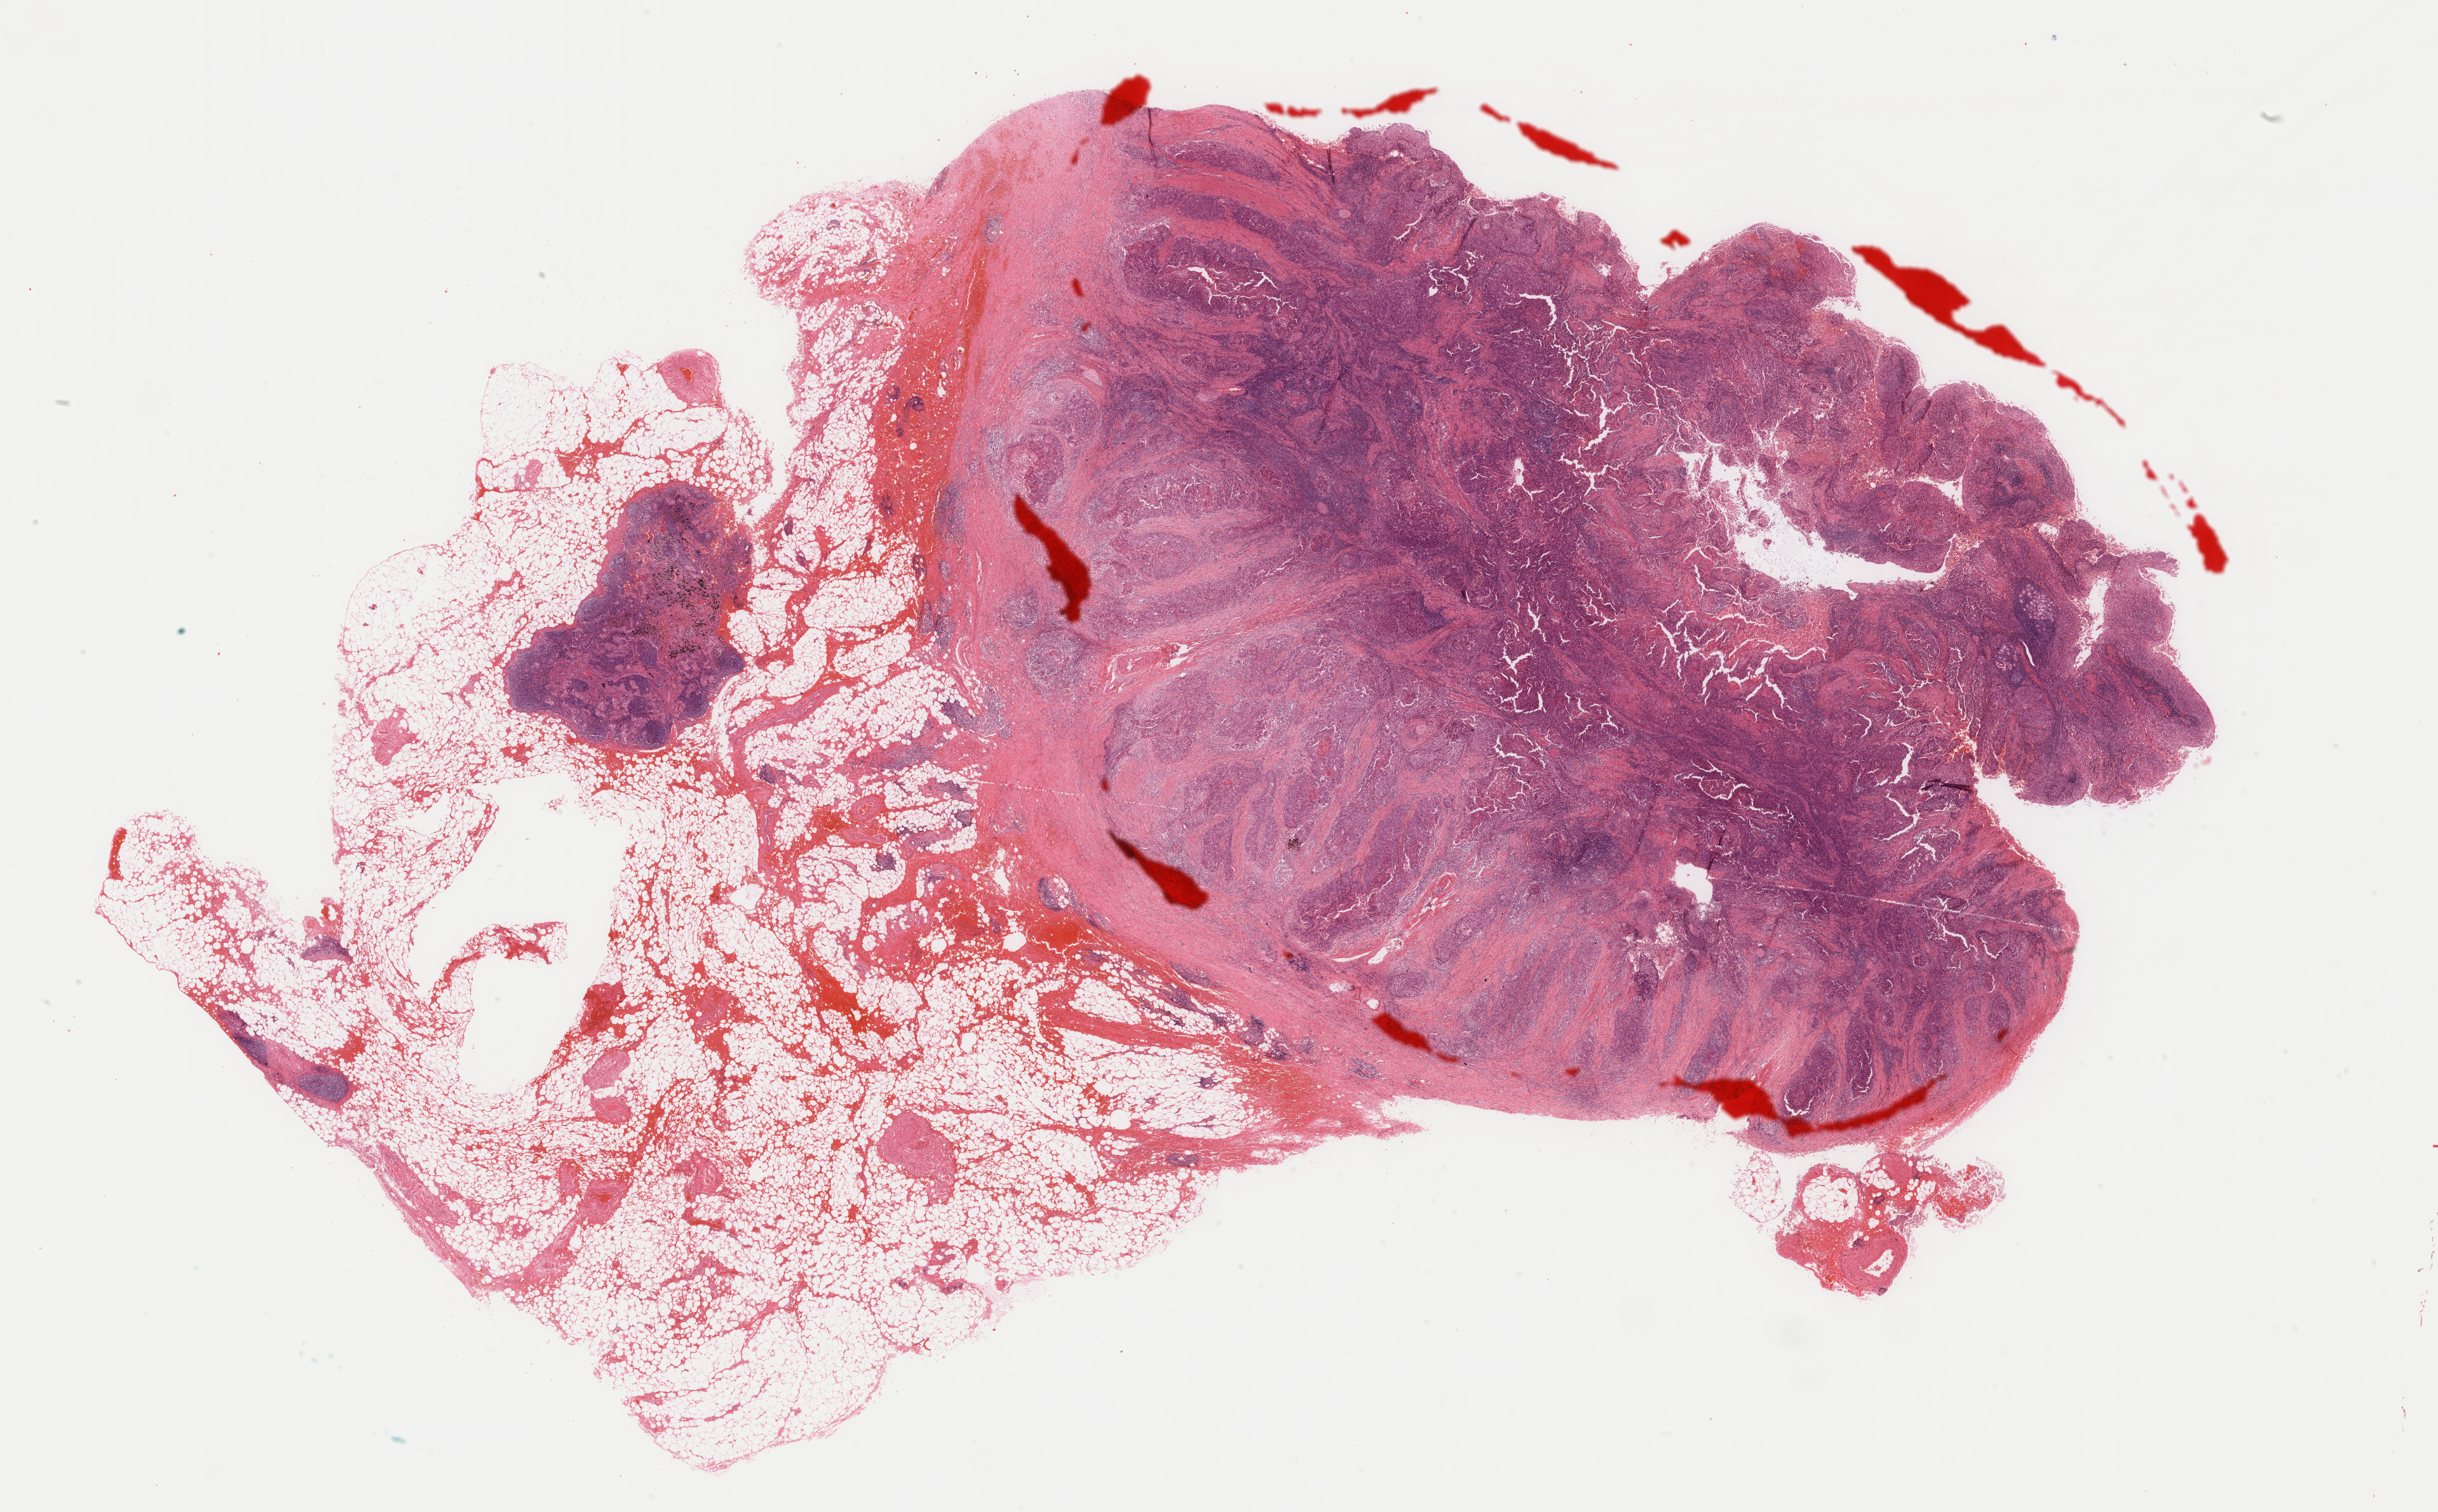
H&E-stained whole-slide image, low-resolution overview of the scanned area, about 30.5 x 18.9 mm (acquisition: 40x scan). Formalin-fixed paraffin-embedded (FFPE) diagnostic section. Esophagus, primary tumour sample. Male patient; age at initial diagnosis 48 years. Histologic grade: G2 (moderately differentiated).
* pathologic diagnosis: Squamous cell carcinoma, NOS (middle third of esophagus)
* AJCC pathologic stage: IIB (7th edition)
* lymph nodes positive (case pathology): 2 of 15 examined